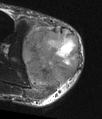
MRI of an extremity soft-tissue mass, one axial slice; slice 24 of 48 in the series (ordered by position); T2-weighted fat-saturated; MR volume resampled by the dataset authors to the PET/CT grid (not the native acquisition matrix); 3.27 mm slice thickness; 102 × 119 image matrix, field of view 100 × 116 mm. Male patient. From the clinical record (not read from this slice): histological type: pleiomorphic liposarcoma; grade: high; site of the primary tumour: right calf.
Outlined on this slice (expert contour drawn on MRI and transferred to this co-registered scan by the dataset authors):
- gross tumour volume including surrounding oedema: box from (x=23, y=21) to (x=81, y=100) px
- gross tumour volume (mass): (x=23, y=28)–(x=81, y=86)